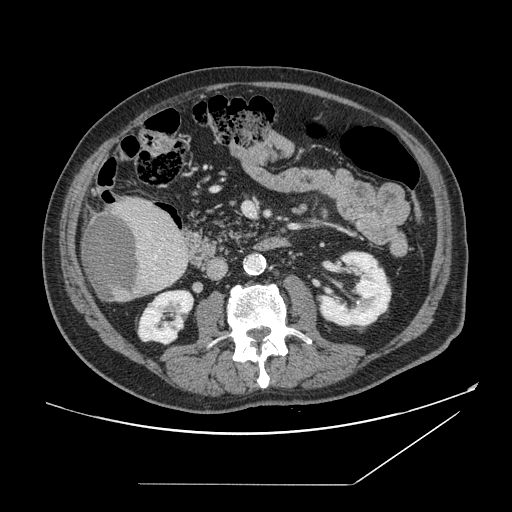
Contrast-enhanced abdominal CT, one axial slice; position 51 of 166 along the scan axis; soft-tissue window (W 400 / L 40 HU); 2.5 mm slice thickness; 512 × 512 image matrix, field of view 416 × 416 mm. Male patient, age 80 years. From the clinical record (not read from this slice): diagnosis: colorectal cancer liver metastases, imaged before liver resection; multiple liver metastases: no; largest metastasis: 2.2 cm; disease in both lobes: no.
Annotated regions visible in this slice (outlined manually by an expert reader):
- liver: bounding box <82,197,189,302> (left, top, right, bottom; pixels)
- liver metastasis: <83,212,140,301>